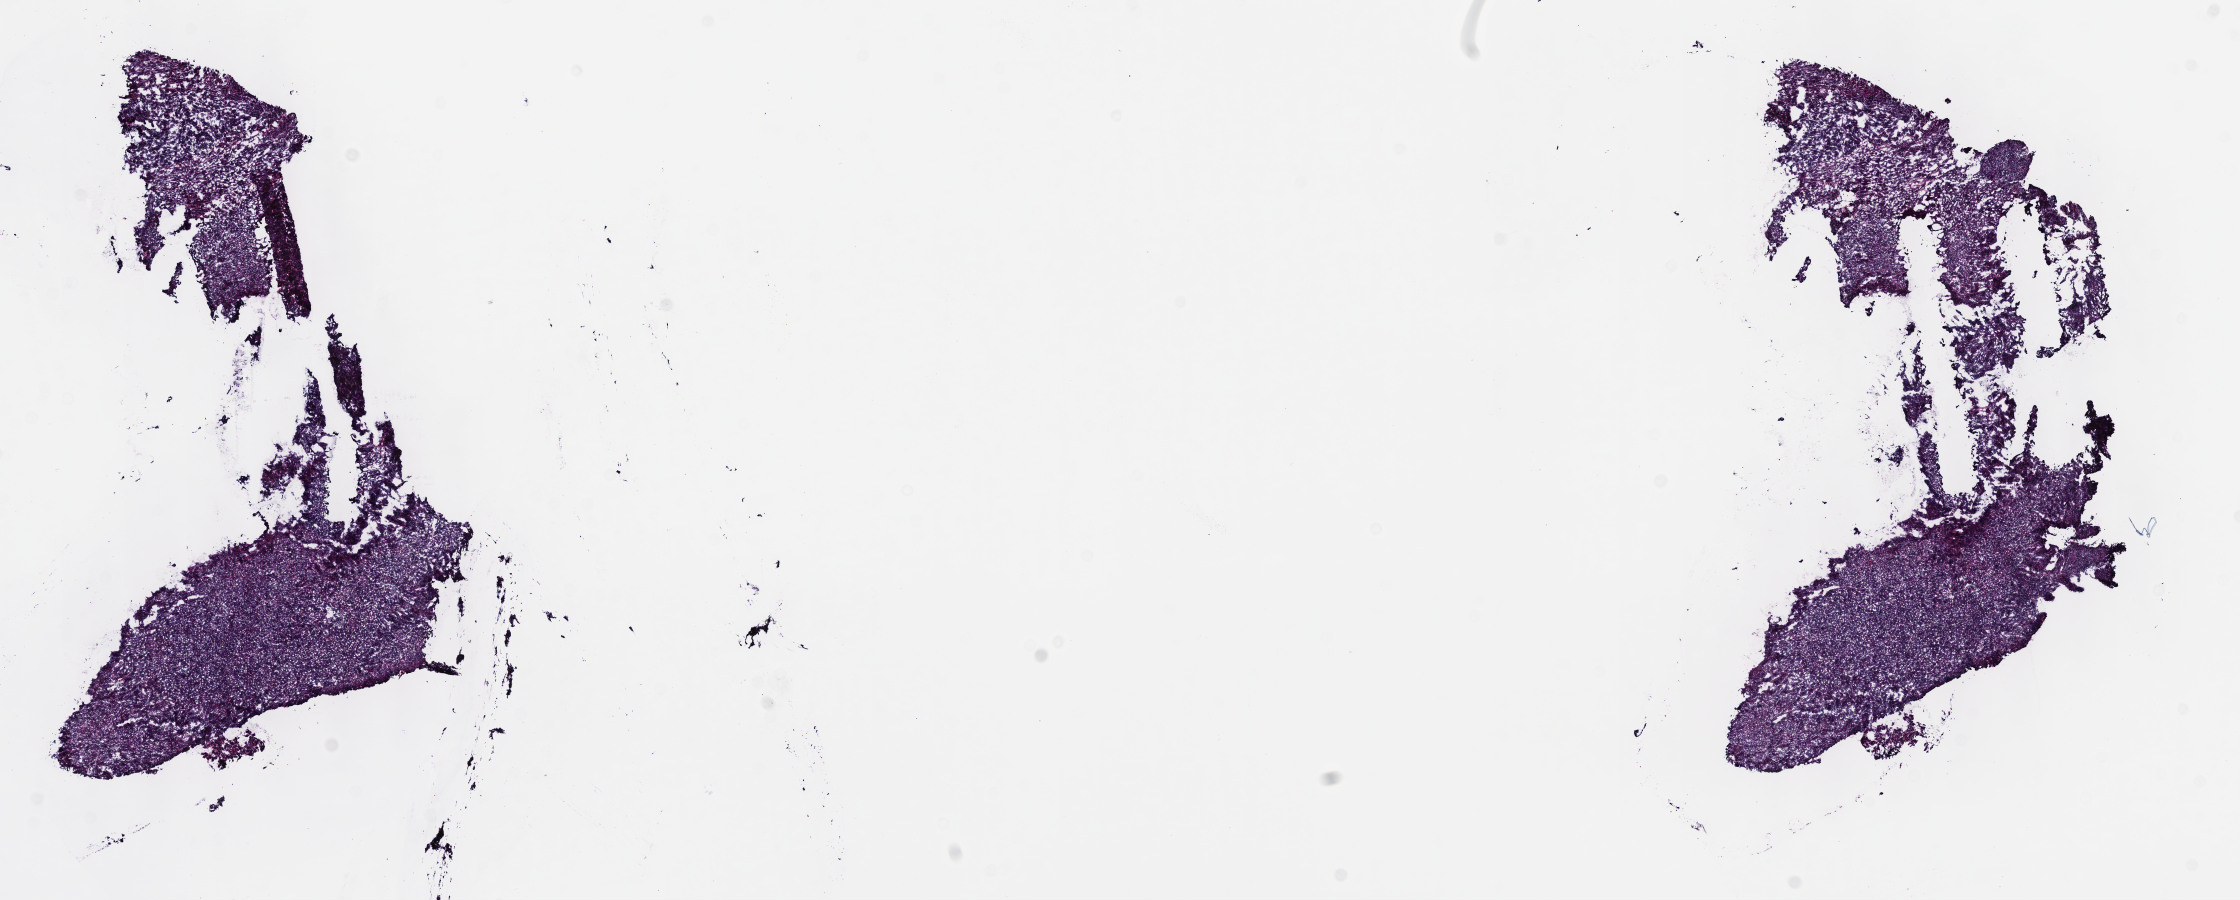
Digitized Hematoxylin and eosin (H&E) stained tissue section (whole slide), shown as a low-resolution overview of the whole scanned area (about 18.1 x 7.3 mm, acquisition: 40x scan), frozen section, sample: primary tumour, thymus. Female, age 76 years at initial diagnosis. Slide review estimates, as recorded: tumour cells 100%, tumour nuclei 80%, normal cells 0%, stromal cells 0%, necrosis 0%. Infiltration values recorded for this section: lymphocyte infiltration 1%, monocyte infiltration 0%, neutrophil infiltration 0%.
Diagnosis: Thymoma, type AB, malignant.